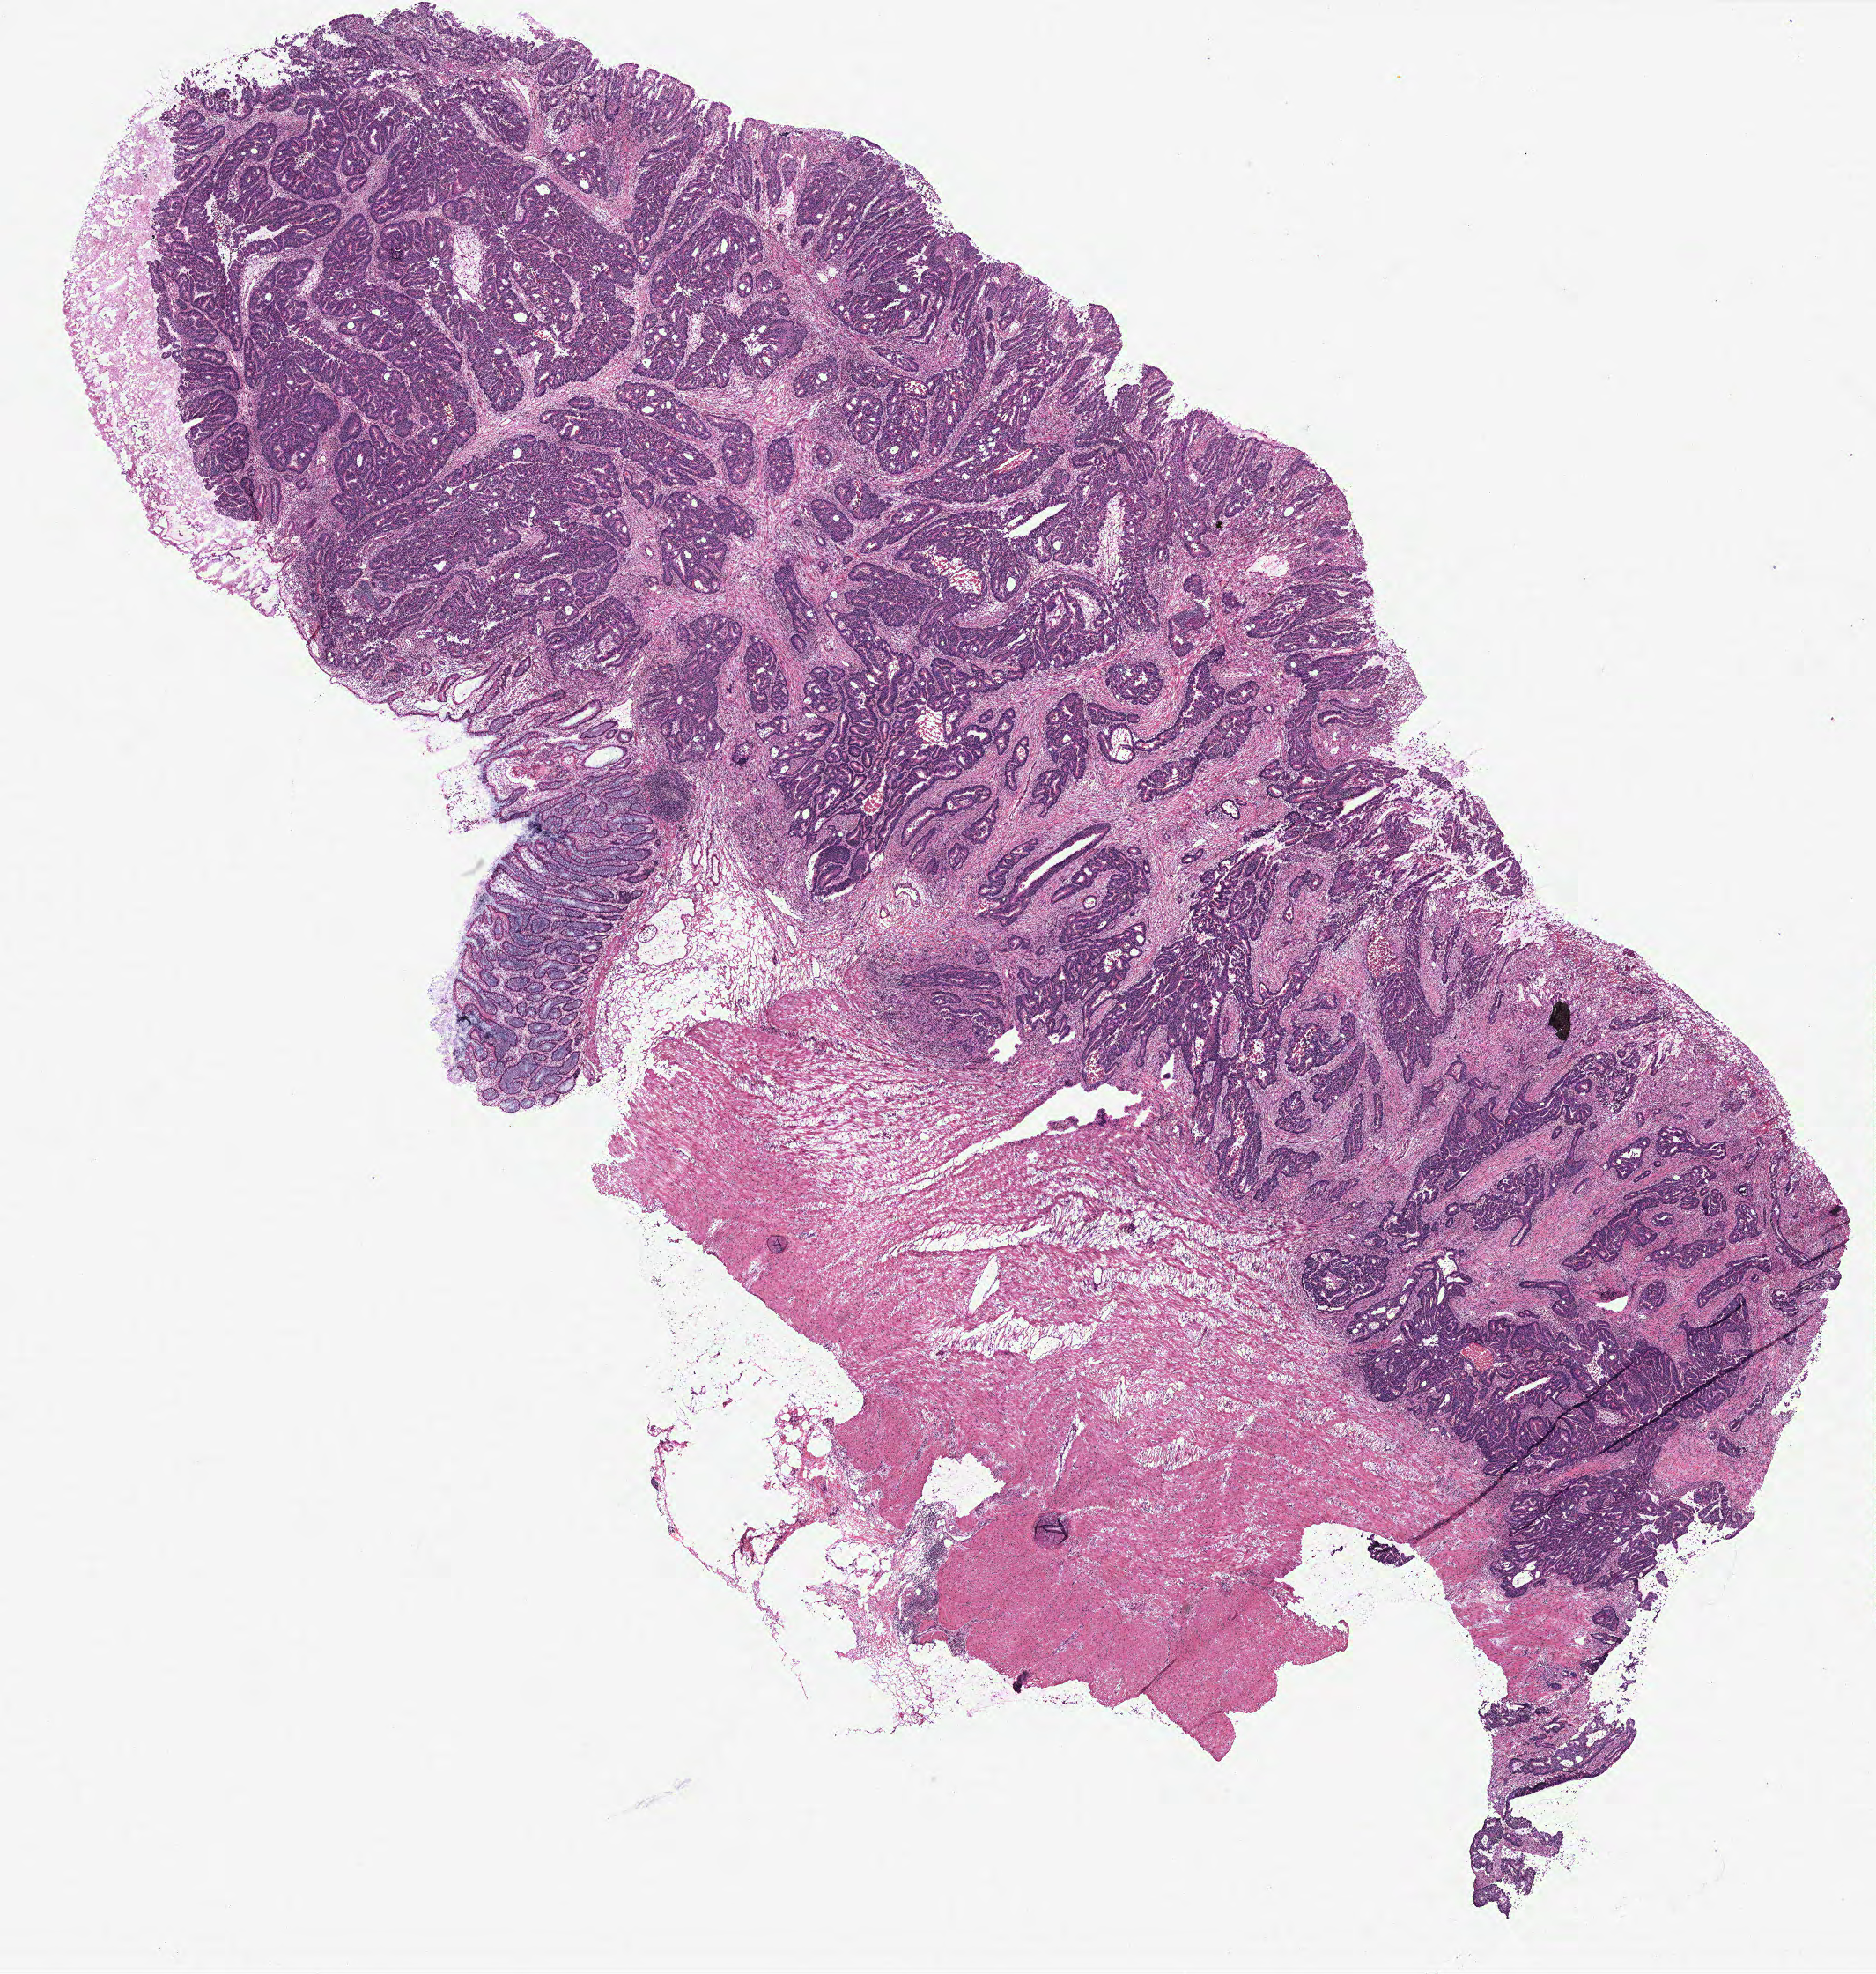
H&E whole-slide image — low-resolution overview of the scanned area, about 17.0 x 17.9 mm (acquisition: 40x scan); normal (non-tumour) tissue sample, colon. Female, 63 y/o.
This section: normal (non-tumour) tissue from the same patient. Patient diagnosis: Adenocarcinoma, NOS.